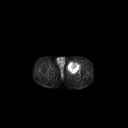
FDG PET of an extremity soft-tissue mass (from a PET/CT study), one axial slice. Slice 260 of 267 in the series (ordered by position). 3.27 mm slice thickness. 128 × 128 image matrix. Male patient, age 63 years. Case-level facts recorded for this patient, not image findings: histological type: pleiomorphic liposarcoma; grade: high; site of the primary tumour: left thigh.
Annotated regions visible in this slice (expert contour drawn on MRI and transferred to this co-registered scan by the dataset authors):
- gross tumour volume including surrounding oedema: bounding box <68,61,80,71> (left, top, right, bottom; pixels)
- gross tumour volume (mass): <68,62,78,71>